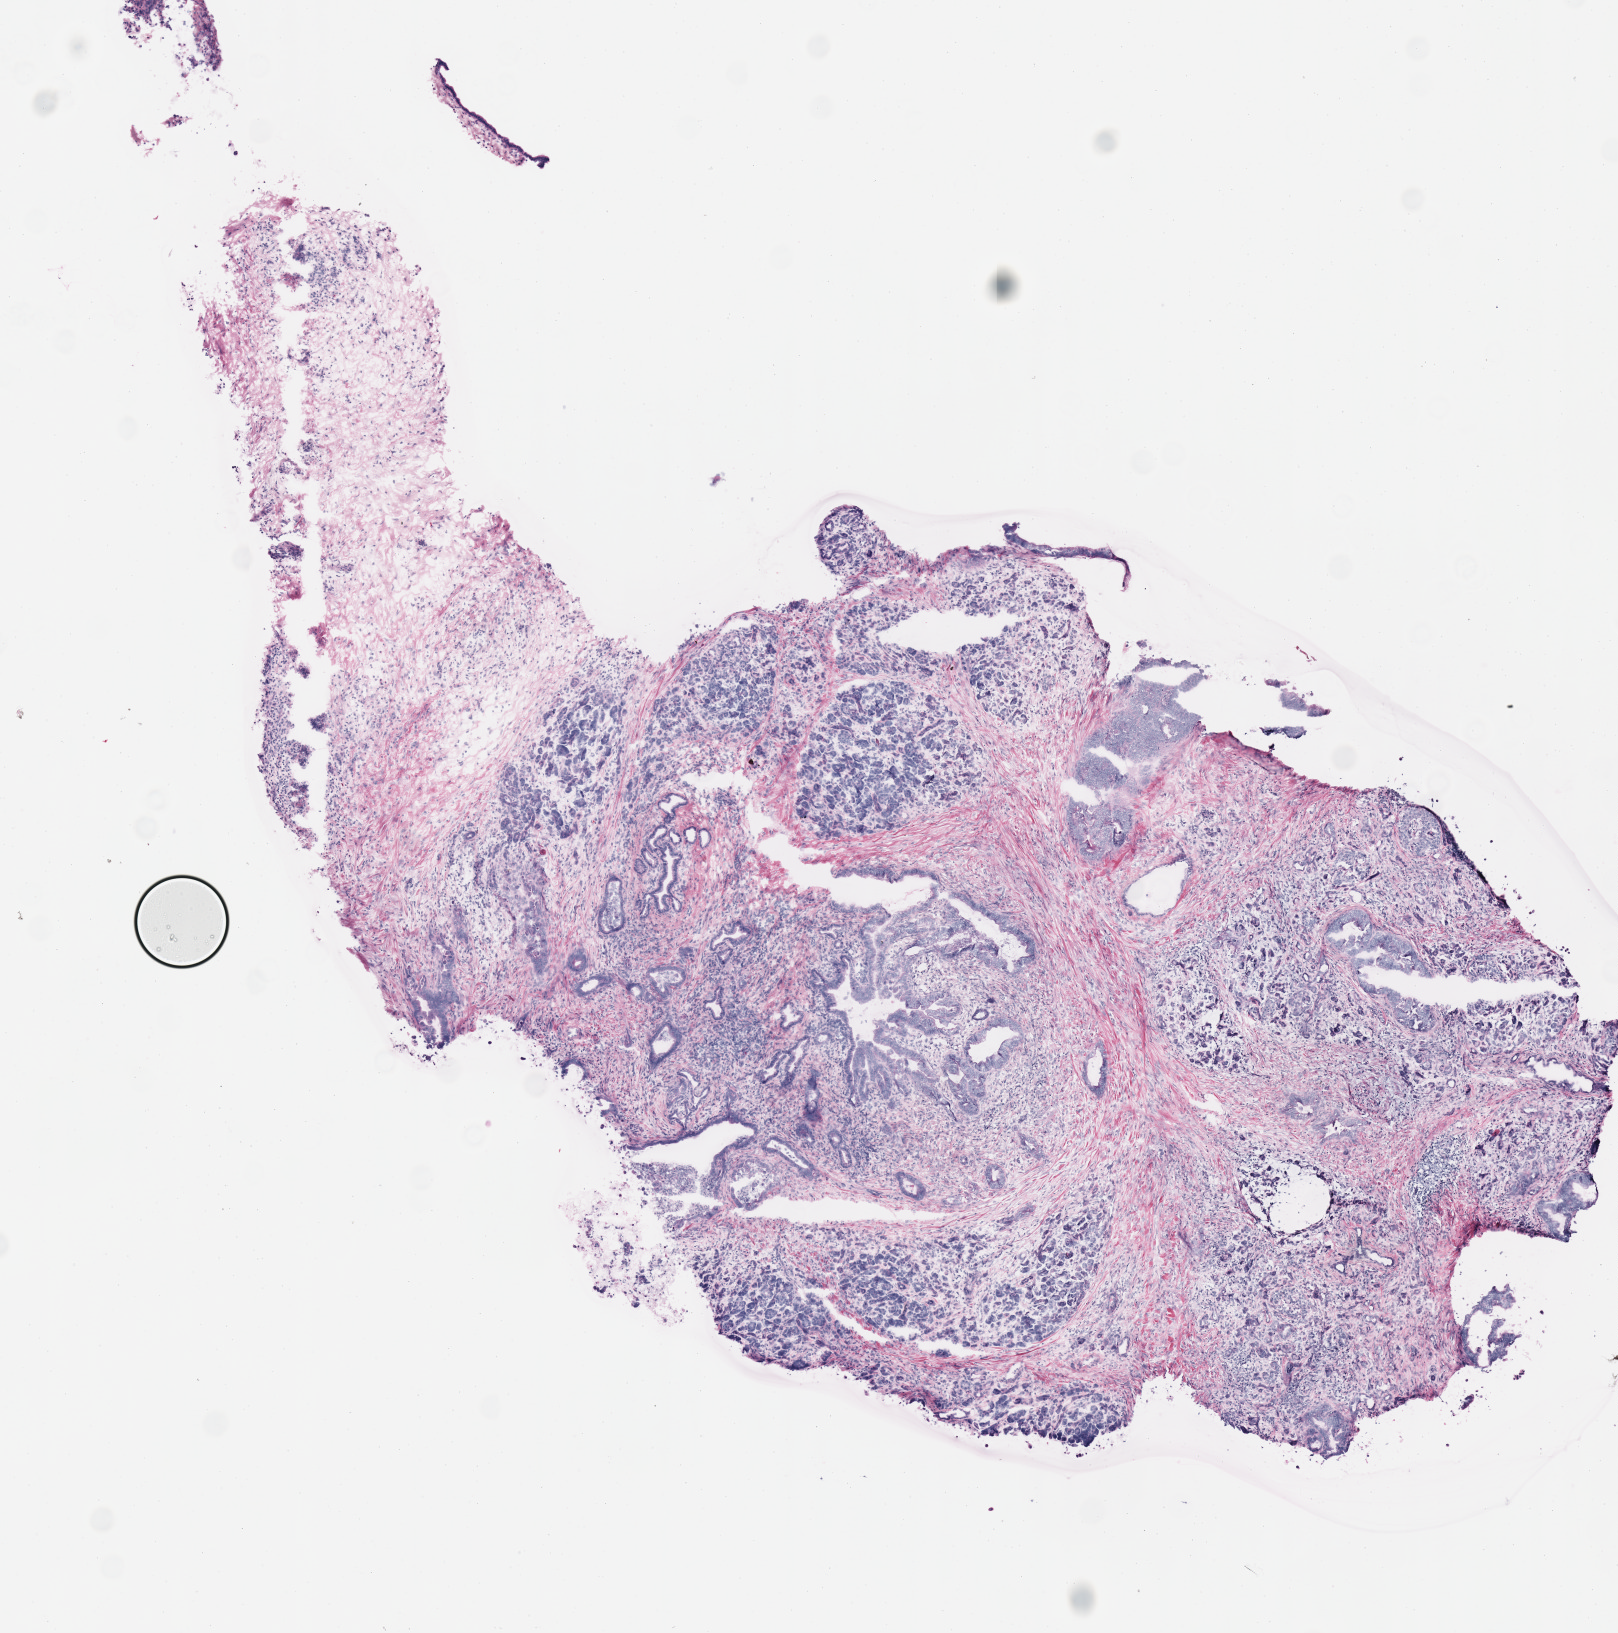
H&E-stained whole-slide image, shown as a low-resolution overview of the whole scanned area (about 6.4 x 6.4 mm, slide scanned at 40x), frozen section from the top of the tissue portion, sample: primary tumour, pancreas. Female, age 49 years at initial diagnosis. Histologic grade: G1 (well differentiated). Composition of this section per pathologist review: tumour cells 75%, tumour nuclei 70%, normal cells 10%, stromal cells 15%, necrosis 0%.
* AJCC pathologic stage: IIB (7th edition)
* lymph nodes positive (case pathology): 7 of 11 examined
* histologic diagnosis: Infiltrating duct carcinoma, NOS